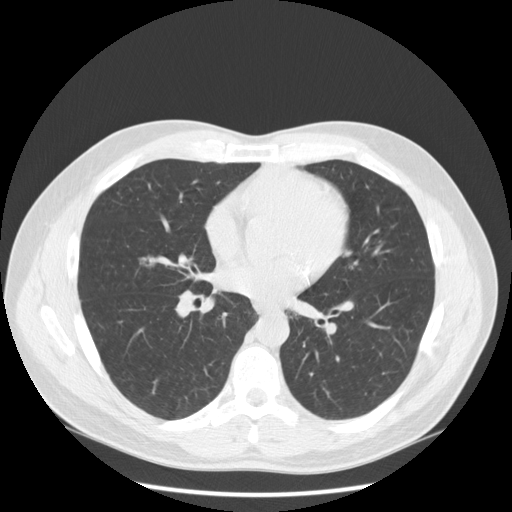
Low-dose screening chest CT, one axial slice. Slice 105 of 234 in the series (ordered by position). Lung window (W 1500 / L -600 HU). 512 × 512 image matrix.
Annotated regions visible in this slice (manually delineated by an expert):
- lesion 1 (tumor, middle lobe of right lung): bounding box (x1, y1, x2, y2) in pixels: (138, 255, 156, 268)